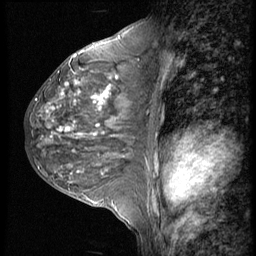
Breast MRI (dynamic contrast-enhanced), one sagittal slice. Slice 27 of 56 in the series (ordered by position). 4 images stored at this slice position (order not interpretable as contrast timing). 1.5 T. TE 4.2 ms, TR 9 ms. 2.5 mm slice thickness. 256 × 256 image matrix. Female patient, age 50 years. Case-level facts recorded for this patient, not image findings: setting: breast cancer imaged before/during neoadjuvant chemotherapy; receptor status: triple-negative.
Outlined on this slice (semi-automatic segmentation, software-assisted and operator-edited):
- analysis volume of interest (the breast-tissue region the enhancement analysis was run in; not a lesion): bounding box (x1, y1, x2, y2) in pixels: (24, 46, 148, 188)
- tumour enhancement mask (voxels above the 140 % enhancement threshold inside the analysis volume of interest): (36, 56, 118, 131)